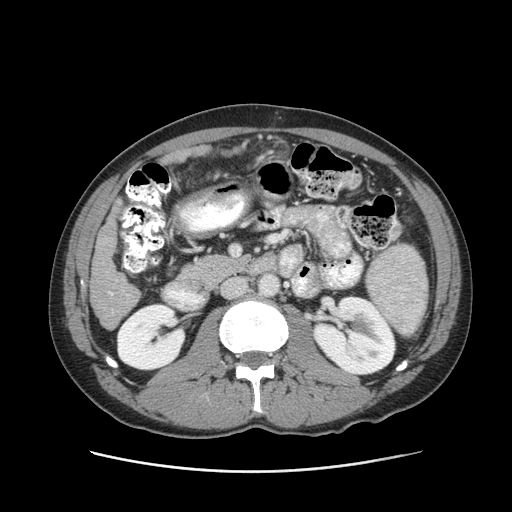
Contrast-enhanced abdominal CT (liver protocol), one axial slice; slice 32 of 93 in the series (ordered by position); 120 kVp; soft-tissue window (W 400 / L 40 HU); 512 × 512 image matrix, field of view 380 × 380 mm. Case-level facts recorded for this patient, not image findings: diagnosis: hepatocellular carcinoma (patient treated with transarterial chemoembolisation; whether this scan precedes or follows treatment is not stated here); TNM stage (as recorded): Stage-II; Child-Pugh class: A.
Structures marked on this image (semi-automatic segmentation, software-assisted and operator-edited):
- liver parenchyma outside the tumour (the mass and vessels are separate outlines, so this box may not span the whole liver): box from (x=90, y=204) to (x=138, y=328) px
- liver vessels: (x=109, y=292)–(x=113, y=295)